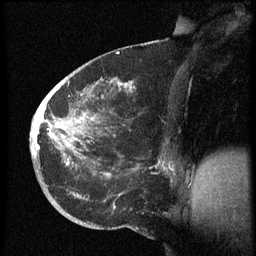
Breast MRI (dynamic contrast-enhanced), one sagittal slice; slice 30 of 60 in the series (ordered by position); dynamic contrast-enhanced series, image 2 of 3 at this slice position (ordered by acquisition); 1.5 T; TE 4.2 ms, TR 8.4 ms; 2.5 mm slice thickness; 256 × 256 image matrix. Patient: female, 38 years. From the clinical record (not read from this slice): setting: breast cancer imaged before/during neoadjuvant chemotherapy; receptor status: HER2-positive.
Outlined on this slice (semi-automatically segmented with operator editing):
- analysis volume of interest (the breast-tissue region the enhancement analysis was run in; not a lesion): bounding box <31,74,173,202> (left, top, right, bottom; pixels)
- tumour enhancement mask (voxels above the 70 % enhancement threshold inside the analysis volume of interest): <33,81,172,176>